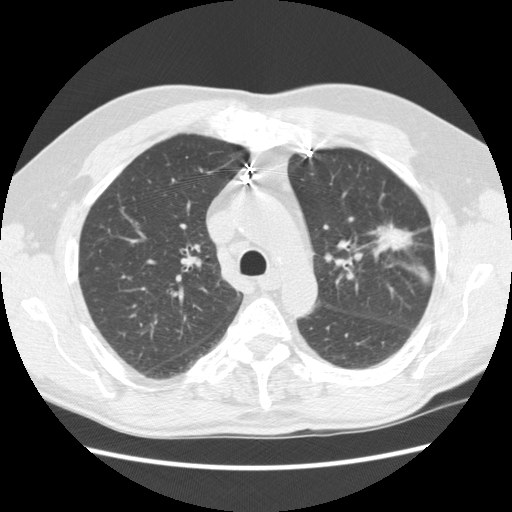
Low-dose screening chest CT, one axial slice. Position 168 of 231 along the scan axis. Reconstruction kernel STANDARD. 120 kVp. Lung window (W 1500 / L -600 HU). 512 × 512 image matrix, field of view 362 × 362 mm.
Structures marked on this image (manually delineated by an expert):
- lesion 1 (tumor, upper lobe of left lung): box from (x=375, y=223) to (x=413, y=252) px